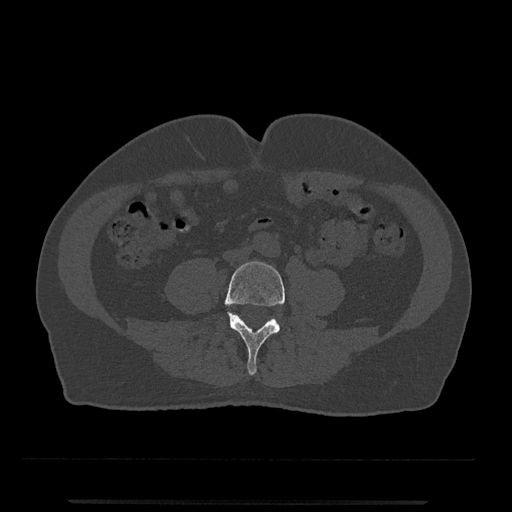
CT including the spine, one axial slice. Slice 130 of 797 in the series (ordered by position). 120 kVp. Bone window (W 1800 / L 400 HU). 0.5 mm slice thickness. 512 × 512 image matrix, field of view 419 × 419 mm. Patient: male, 63 years. Case-level facts recorded for this patient, not image findings: primary cancer: prostate.
Structures marked on this image (semi-automatic segmentation, software-assisted and operator-edited):
- L4 vertebra: bounding box (x1, y1, x2, y2) in pixels: (224, 261, 285, 375)